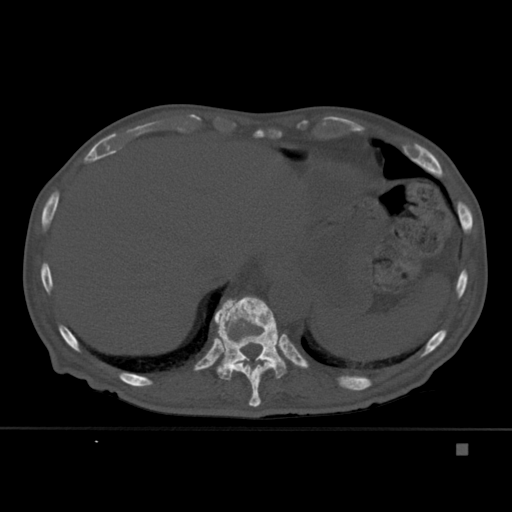
CT including the spine, one axial slice. Bone window (W 1800 / L 400 HU). 1.5 mm slice thickness. 512 × 512 image matrix. Male patient, age 75 years. Case-level facts recorded for this patient, not image findings: primary cancer: prostate.
Annotated regions visible in this slice (semi-automatic segmentation, software-assisted and operator-edited):
- T10 vertebra: box from (x=233, y=356) to (x=285, y=407) px
- T11 vertebra: (x=213, y=296)–(x=287, y=381)